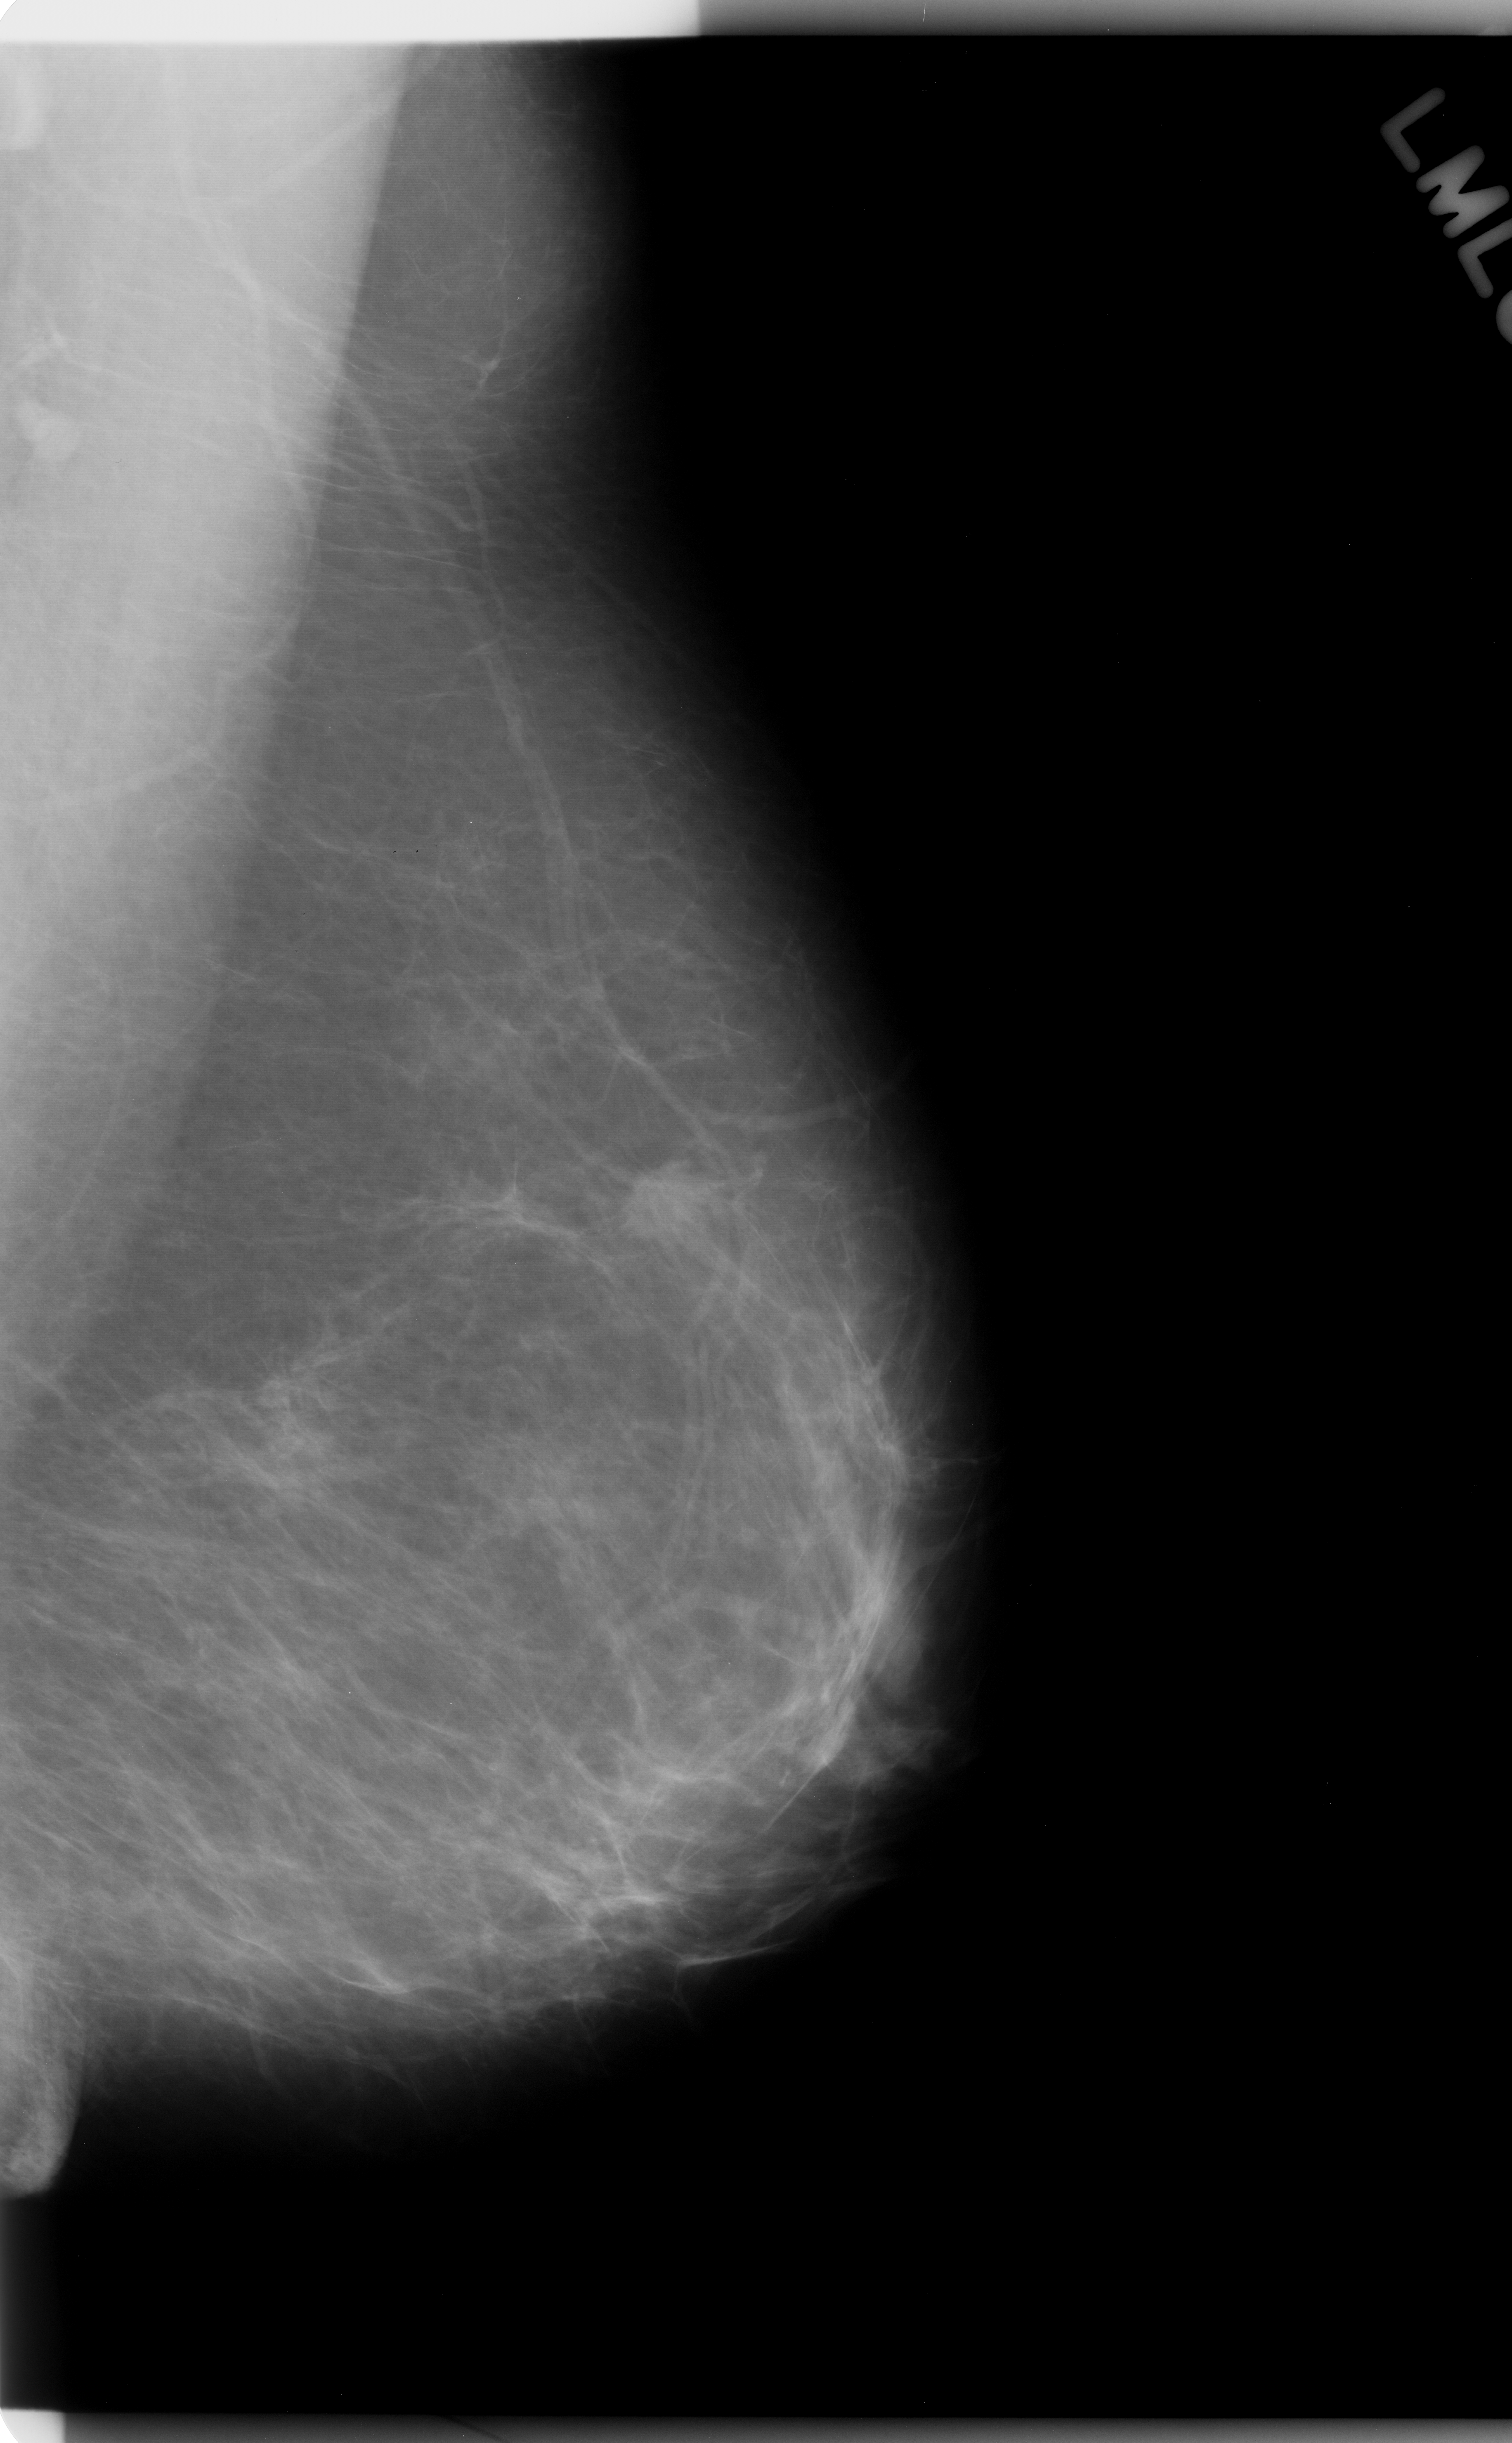
Scanned film-screen mammogram. Left breast. MLO view. 1512 × 2443 image matrix.
Marked abnormalities (boxes around the expert regions of interest):
- mass, shape oval, margins spiculated; BI-RADS assessment category 5; pathology result (as recorded, not read from the image): malignant: box from (x=611, y=1156) to (x=735, y=1258) px